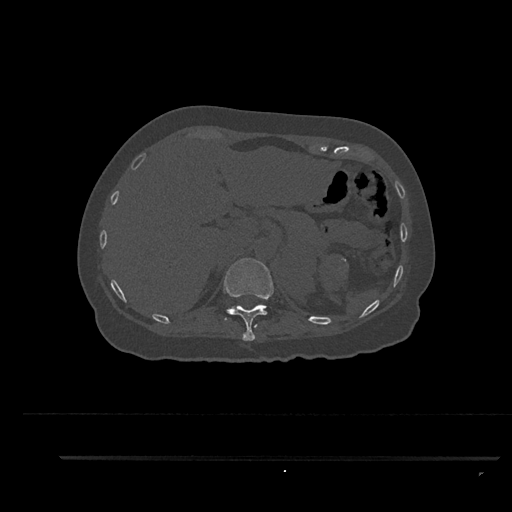
CT including the spine, one axial slice. Position 307 of 797 along the scan axis. Reconstruction kernel Br40s/3. 120 kVp. Bone window (W 1800 / L 400 HU). 512 × 512 image matrix. Patient: female, 44 years. Case-level facts recorded for this patient, not image findings: primary cancer: renal.
Structures marked on this image (semi-automatic segmentation, software-assisted and operator-edited):
- T11 vertebra: bounding box <224,258,274,341> (left, top, right, bottom; pixels)
- T12 vertebra: <224,307,232,320>